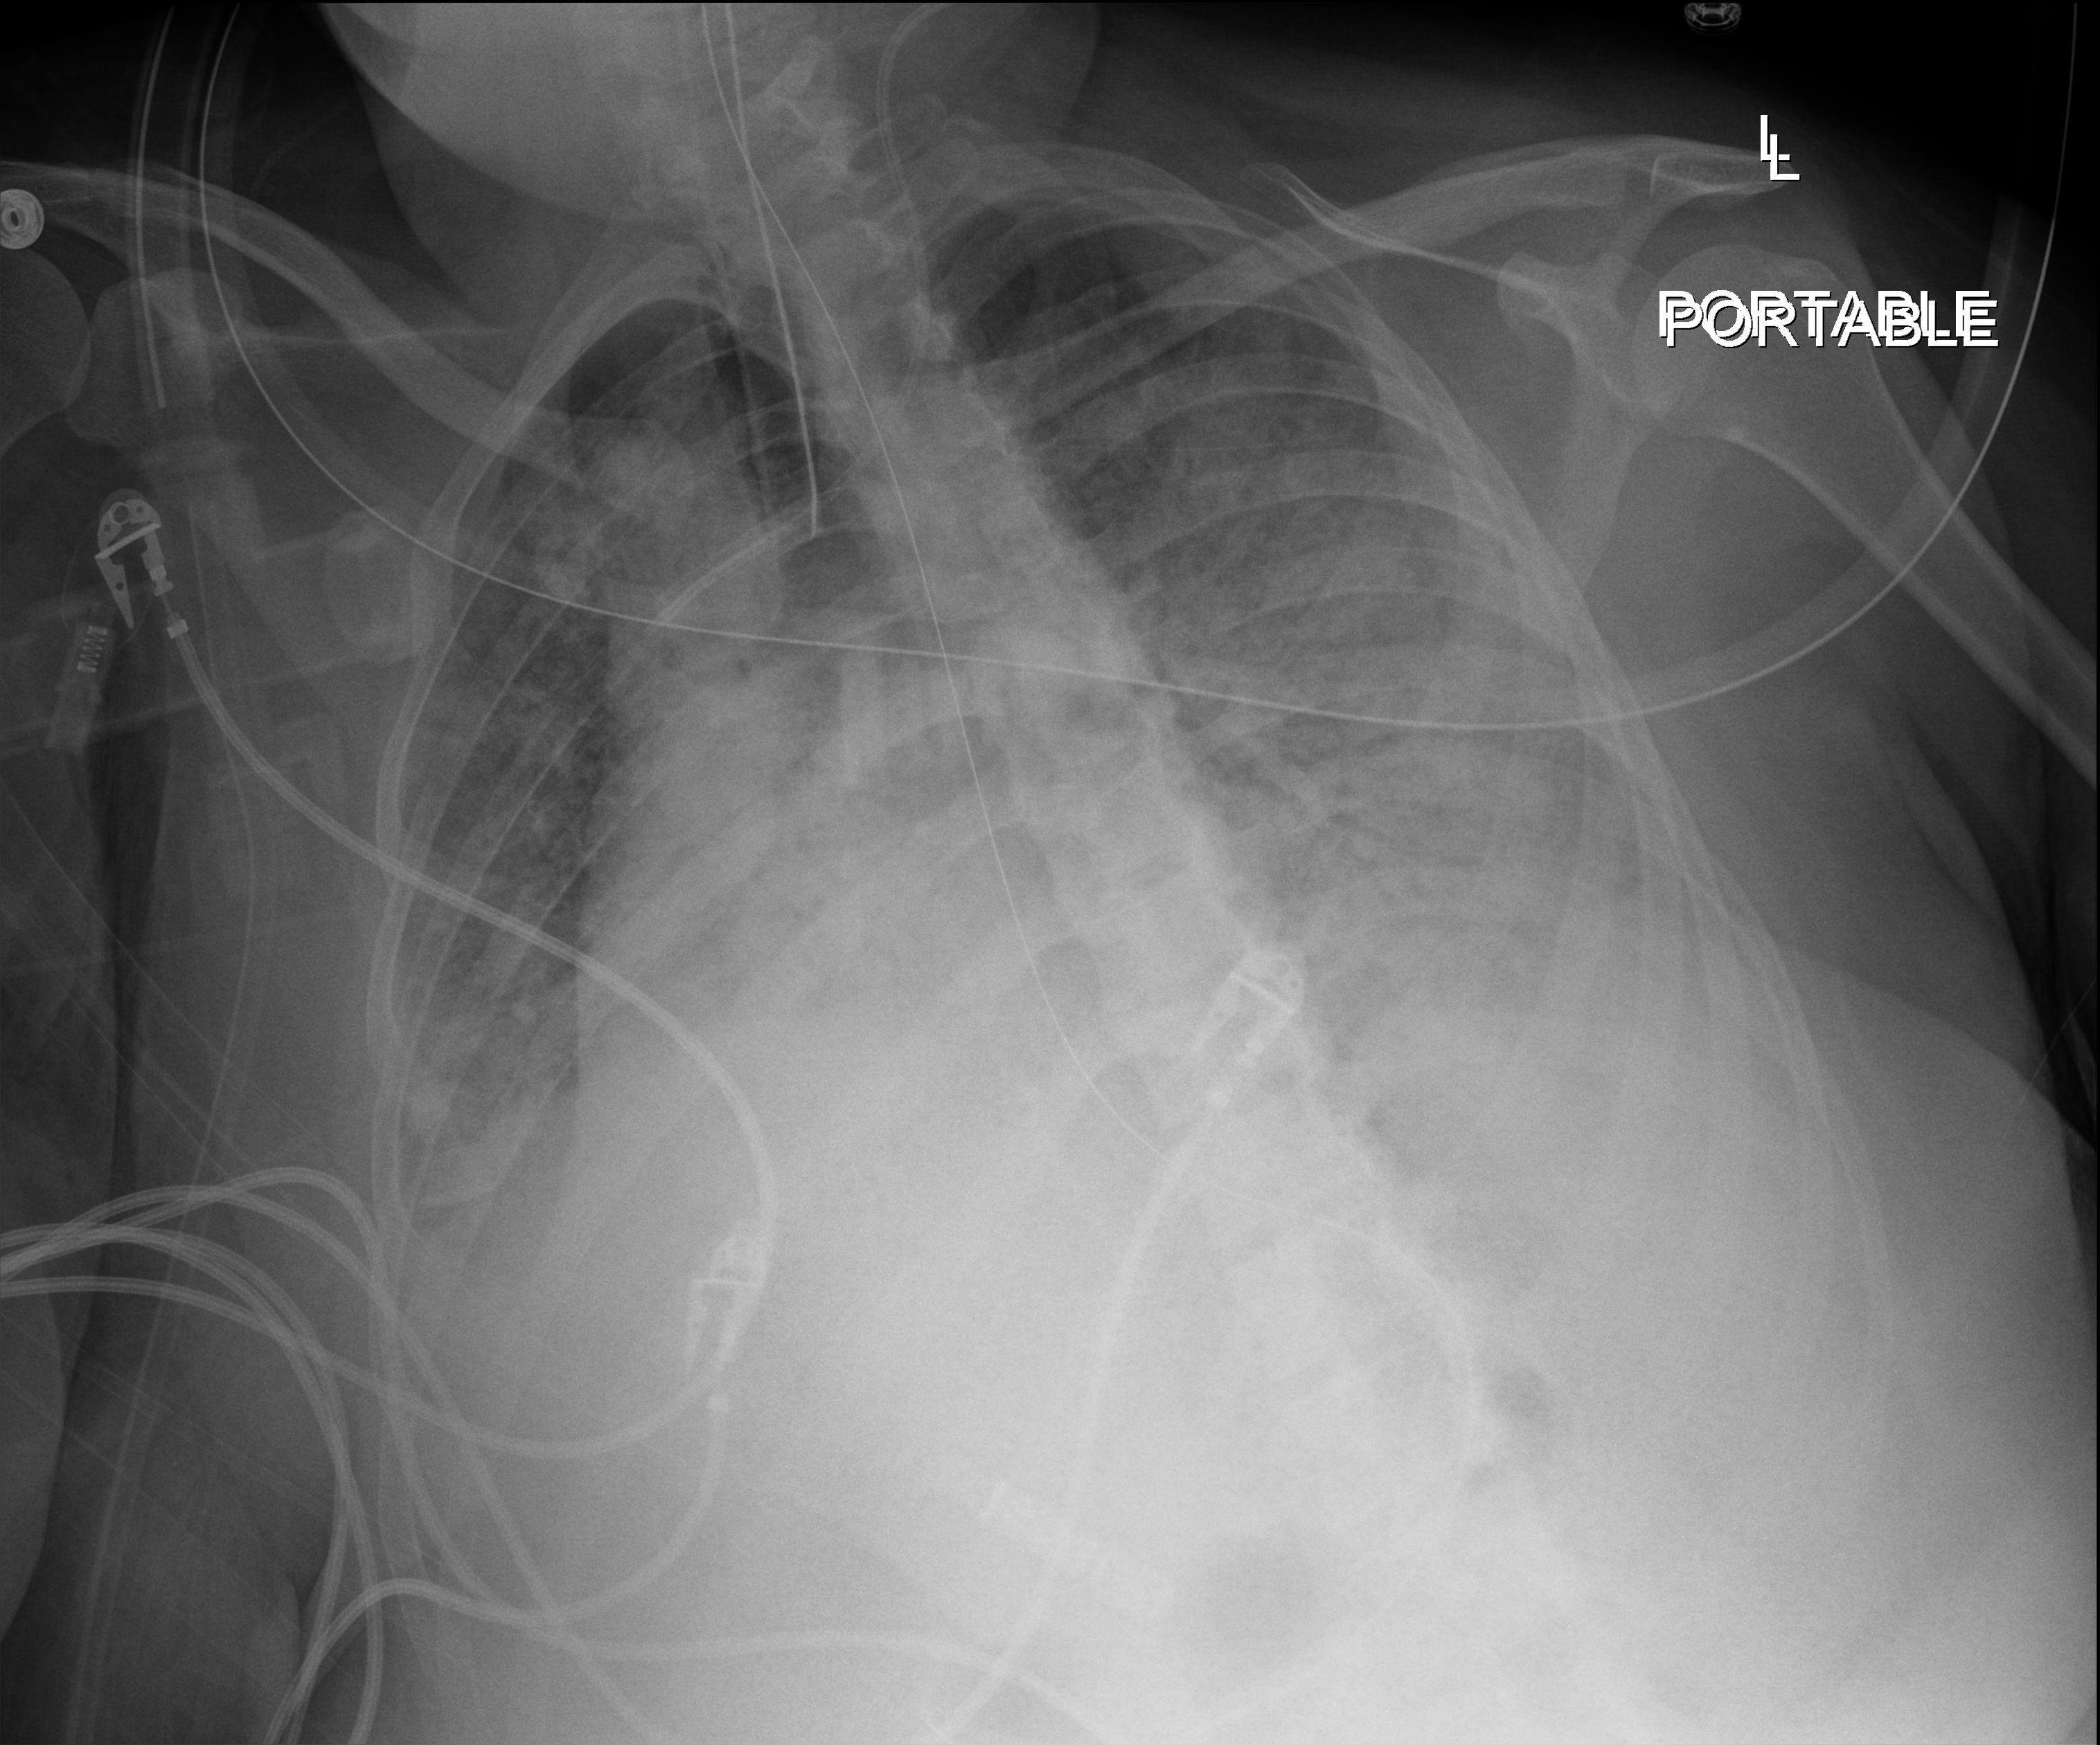
Chest X-ray; anteroposterior (AP) projection. Patient hospitalised with COVID-19; female, aged 18–59 years.
Admission-level facts for this patient (not findings on this image; timing relative to this image not recorded): admitted to intensive care during this hospital stay: no; length of hospital stay: 33 days.